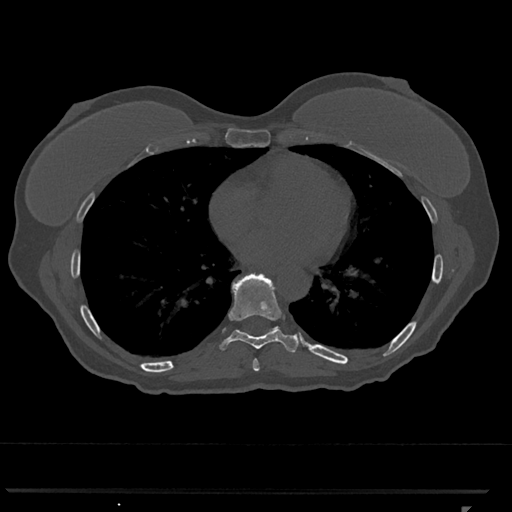
CT including the spine, one axial slice; position 661 of 793 along the scan axis; reconstruction kernel Br40s/3; 120 kVp; bone window (W 1800 / L 400 HU); 0.5 mm slice thickness; 512 × 512 image matrix, field of view 380 × 380 mm. Patient: female, 62 years. Case-level facts recorded for this patient, not image findings: primary cancer: renal.
Annotated regions visible in this slice (semi-automatic segmentation, software-assisted and operator-edited):
- T7 vertebra: bounding box [x1, y1, x2, y2] px = [253, 359, 260, 371]
- T8 vertebra: [219, 274, 300, 352]
- T9 vertebra: [237, 326, 279, 330]